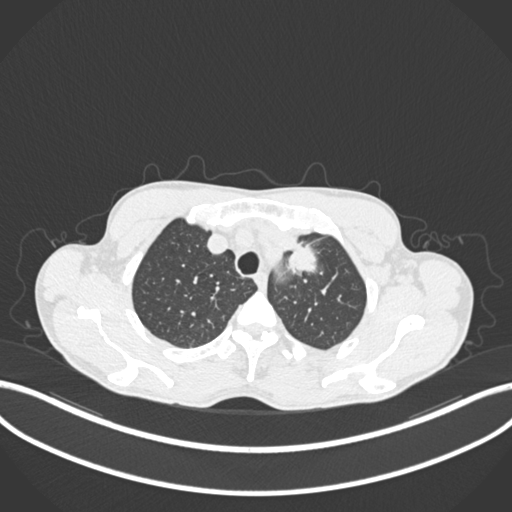
Chest CT, one axial slice. Slice 170 of 211 in the series (ordered by position). Lung window (W 1500 / L -600 HU). 1 mm slice thickness. 512 × 512 image matrix, field of view 400 × 400 mm. Male patient, age 58 years. Case-level facts recorded for this patient, not image findings: clinical TNM (as recorded): T1c N1 M0.
Structures marked on this image (bounding box drawn by a radiologist):
- lung tumour (recorded histology: adenocarcinoma): bounding box (x1, y1, x2, y2) in pixels: (278, 241, 325, 283)